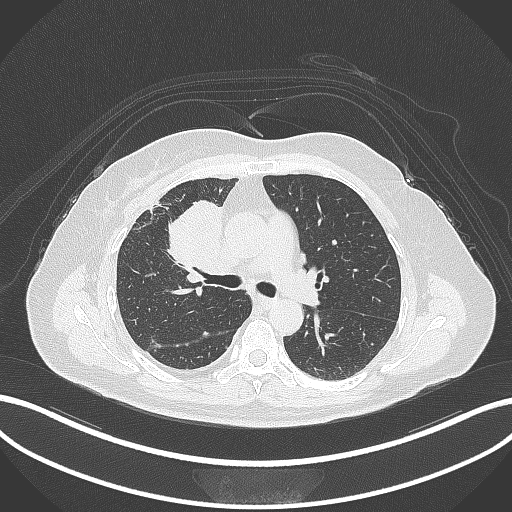
Chest CT, one axial slice; position 174 of 305 along the scan axis; 120 kVp; lung window (W 1500 / L -600 HU); 1 mm slice thickness; 512 × 512 image matrix. Patient: female, 52 years. From the clinical record (not read from this slice): clinical TNM (as recorded): T3 N1 M1.
Structures marked on this image (rectangle marked by the reading radiologist):
- lung tumour (recorded histology: adenocarcinoma): bounding box [x1, y1, x2, y2] px = [164, 193, 230, 277]